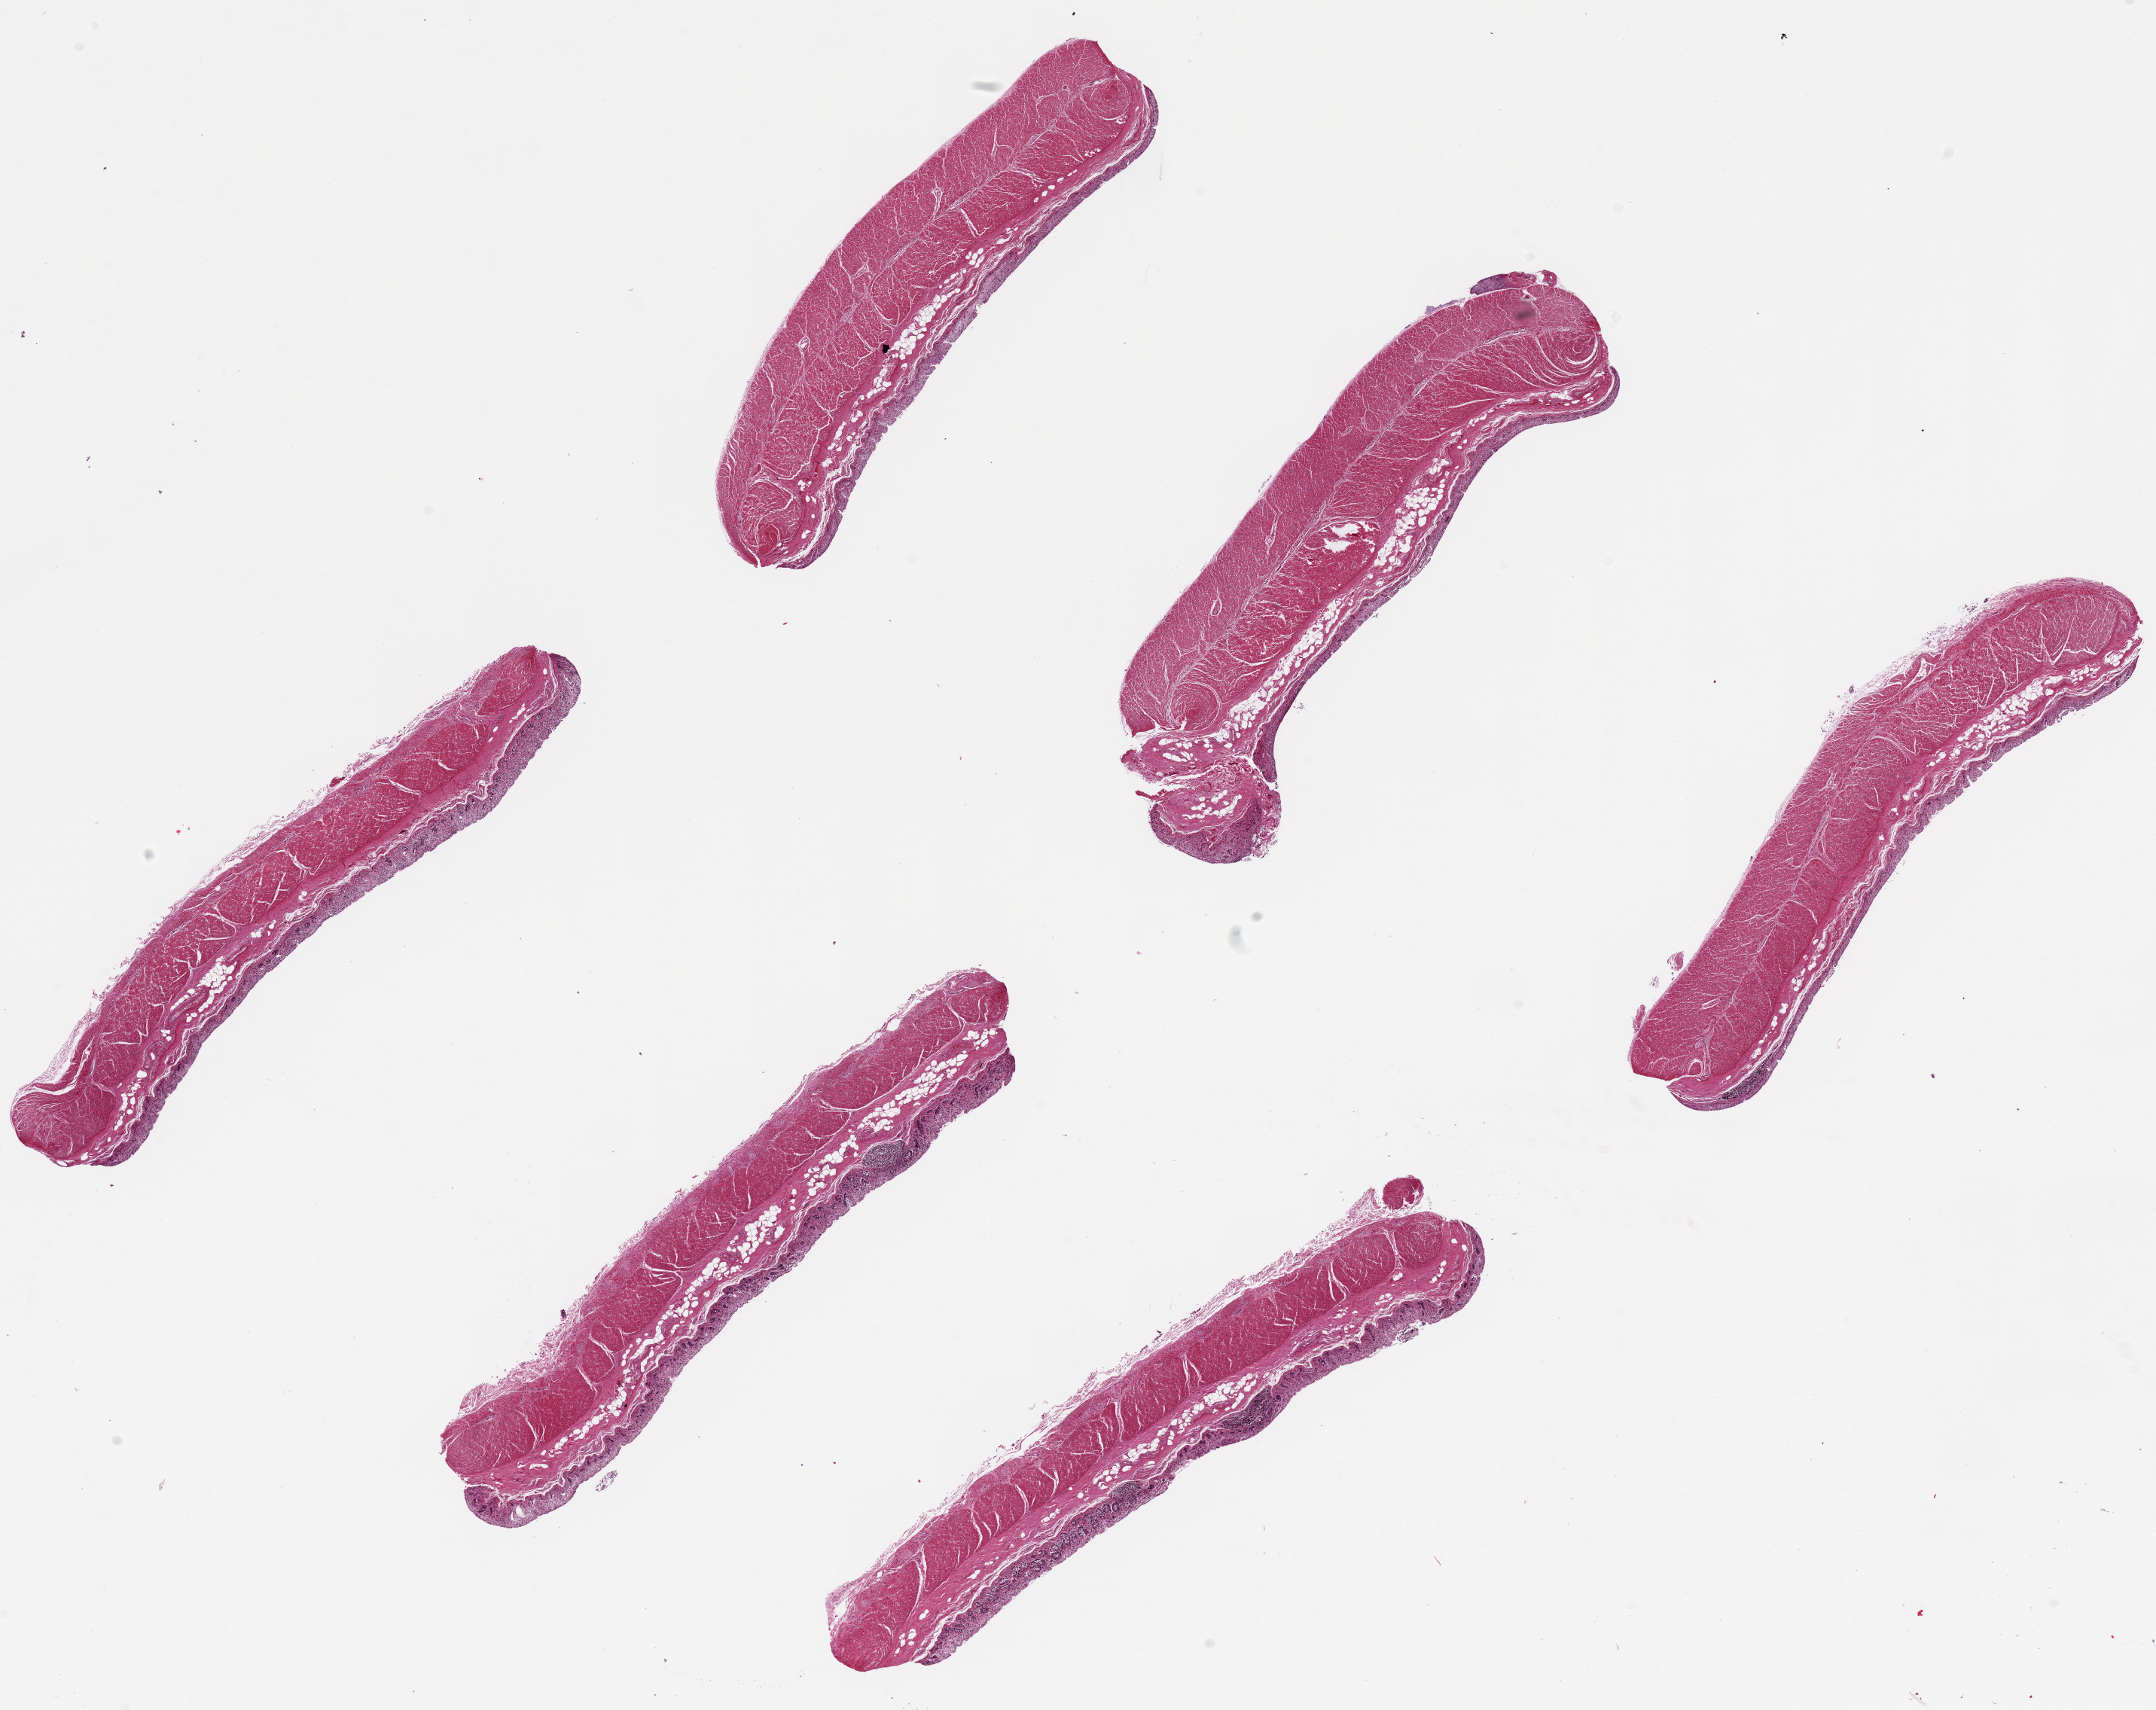
H&E whole-slide image, shown as a low-resolution overview of the whole scanned area (about 22.6 x 18.0 mm); PAXgene-fixed paraffin-embedded (PFPE) section; section of transverse colon (target tissue); tissue donor sample. Male donor.
Reviewer comment on this tissue sample: 6 pieces, ~7.5x1.5mm. Mucosa badly autolyzed, 10-20% of thickness.